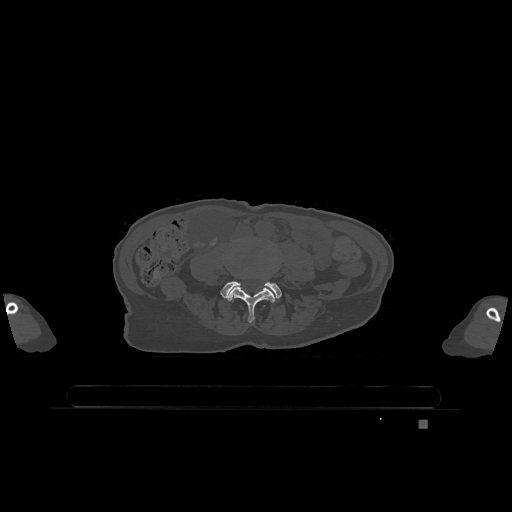
CT including the spine, one axial slice; position 274 of 1317 along the scan axis; bone window (W 1800 / L 400 HU); 0.5 mm slice thickness; 512 × 512 image matrix, field of view 500 × 500 mm. Female patient, age 74 years. Case-level facts recorded for this patient, not image findings: primary cancer: lung; vertebrae with lytic lesions (as recorded): T1, T4, T5, T6, L4, L5.
Outlined on this slice (semi-automatically segmented with operator editing):
- L4 vertebra: bounding box <228,287,275,323> (left, top, right, bottom; pixels)
- L5 vertebra: <220,281,282,301>